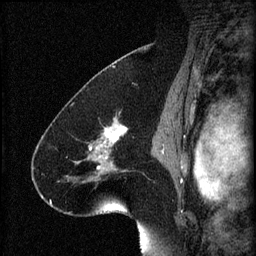
Breast MRI (dynamic contrast-enhanced), one sagittal slice. Slice 42 of 60 in the series (ordered by position). 3 images stored at this slice position (order not interpretable as contrast timing). 1.5 T. TE 4.2 ms, TR 8.2 ms. 2 mm slice thickness. 256 × 256 image matrix, field of view 180 × 180 mm. Female patient, age 41 years.
Annotated regions visible in this slice (semi-automatic segmentation, software-assisted and operator-edited):
- analysis volume of interest (the breast-tissue region the enhancement analysis was run in; not a lesion): bounding box (x1, y1, x2, y2) in pixels: (72, 120, 133, 185)
- tumour enhancement mask (voxels above the 70 % enhancement threshold inside the analysis volume of interest): (90, 124, 128, 173)